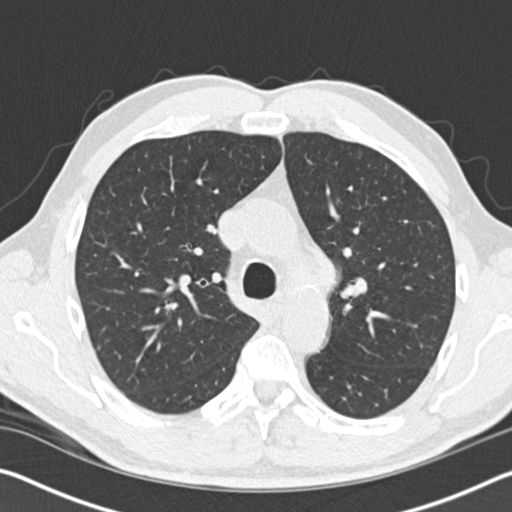
Chest CT (low-dose screening protocol), one axial image; baseline screening round; lung window (W 1500 / L -600 HU); standard (soft-tissue) reconstruction kernel (B30f); 512 × 512 image matrix, field of view 340 × 340 mm. Male participant, aged 61 years at enrolment. Former smoker at enrolment.
Expert-annotated lung lesion, bounding box [x1, y1, x2, y2] px = [344, 275, 373, 314]. The screening reader recorded 2 non-calcified nodules or masses ≥4 mm on this exam; which of them this box marks is not recorded. Participant outcome: lung cancer diagnosed 183 days after this screen — small cell carcinoma, NOS, left upper lobe, stage IIIB (AJCC 6th edition), 100 mm at pathology.